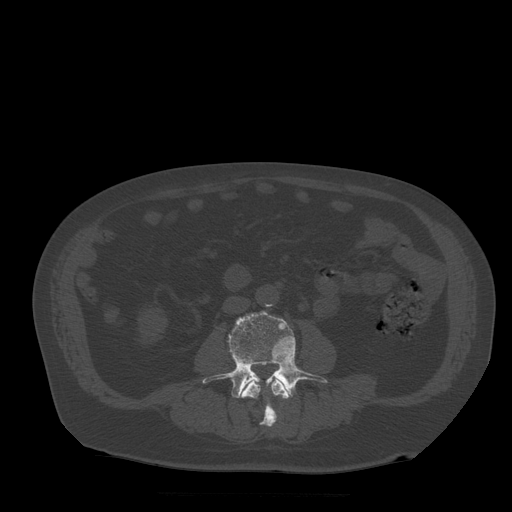
CT including the spine, one axial slice. Position 123 of 522 along the scan axis. Bone window (W 1800 / L 400 HU). 1.25 mm slice thickness. 512 × 512 image matrix, field of view 420 × 420 mm. Patient age 72 years. From the clinical record (not read from this slice): primary cancer: prostate.
Outlined on this slice (semi-automatically segmented with operator editing):
- L3 vertebra: bounding box (x1, y1, x2, y2) in pixels: (240, 379, 290, 428)
- L4 vertebra: (203, 311, 328, 421)